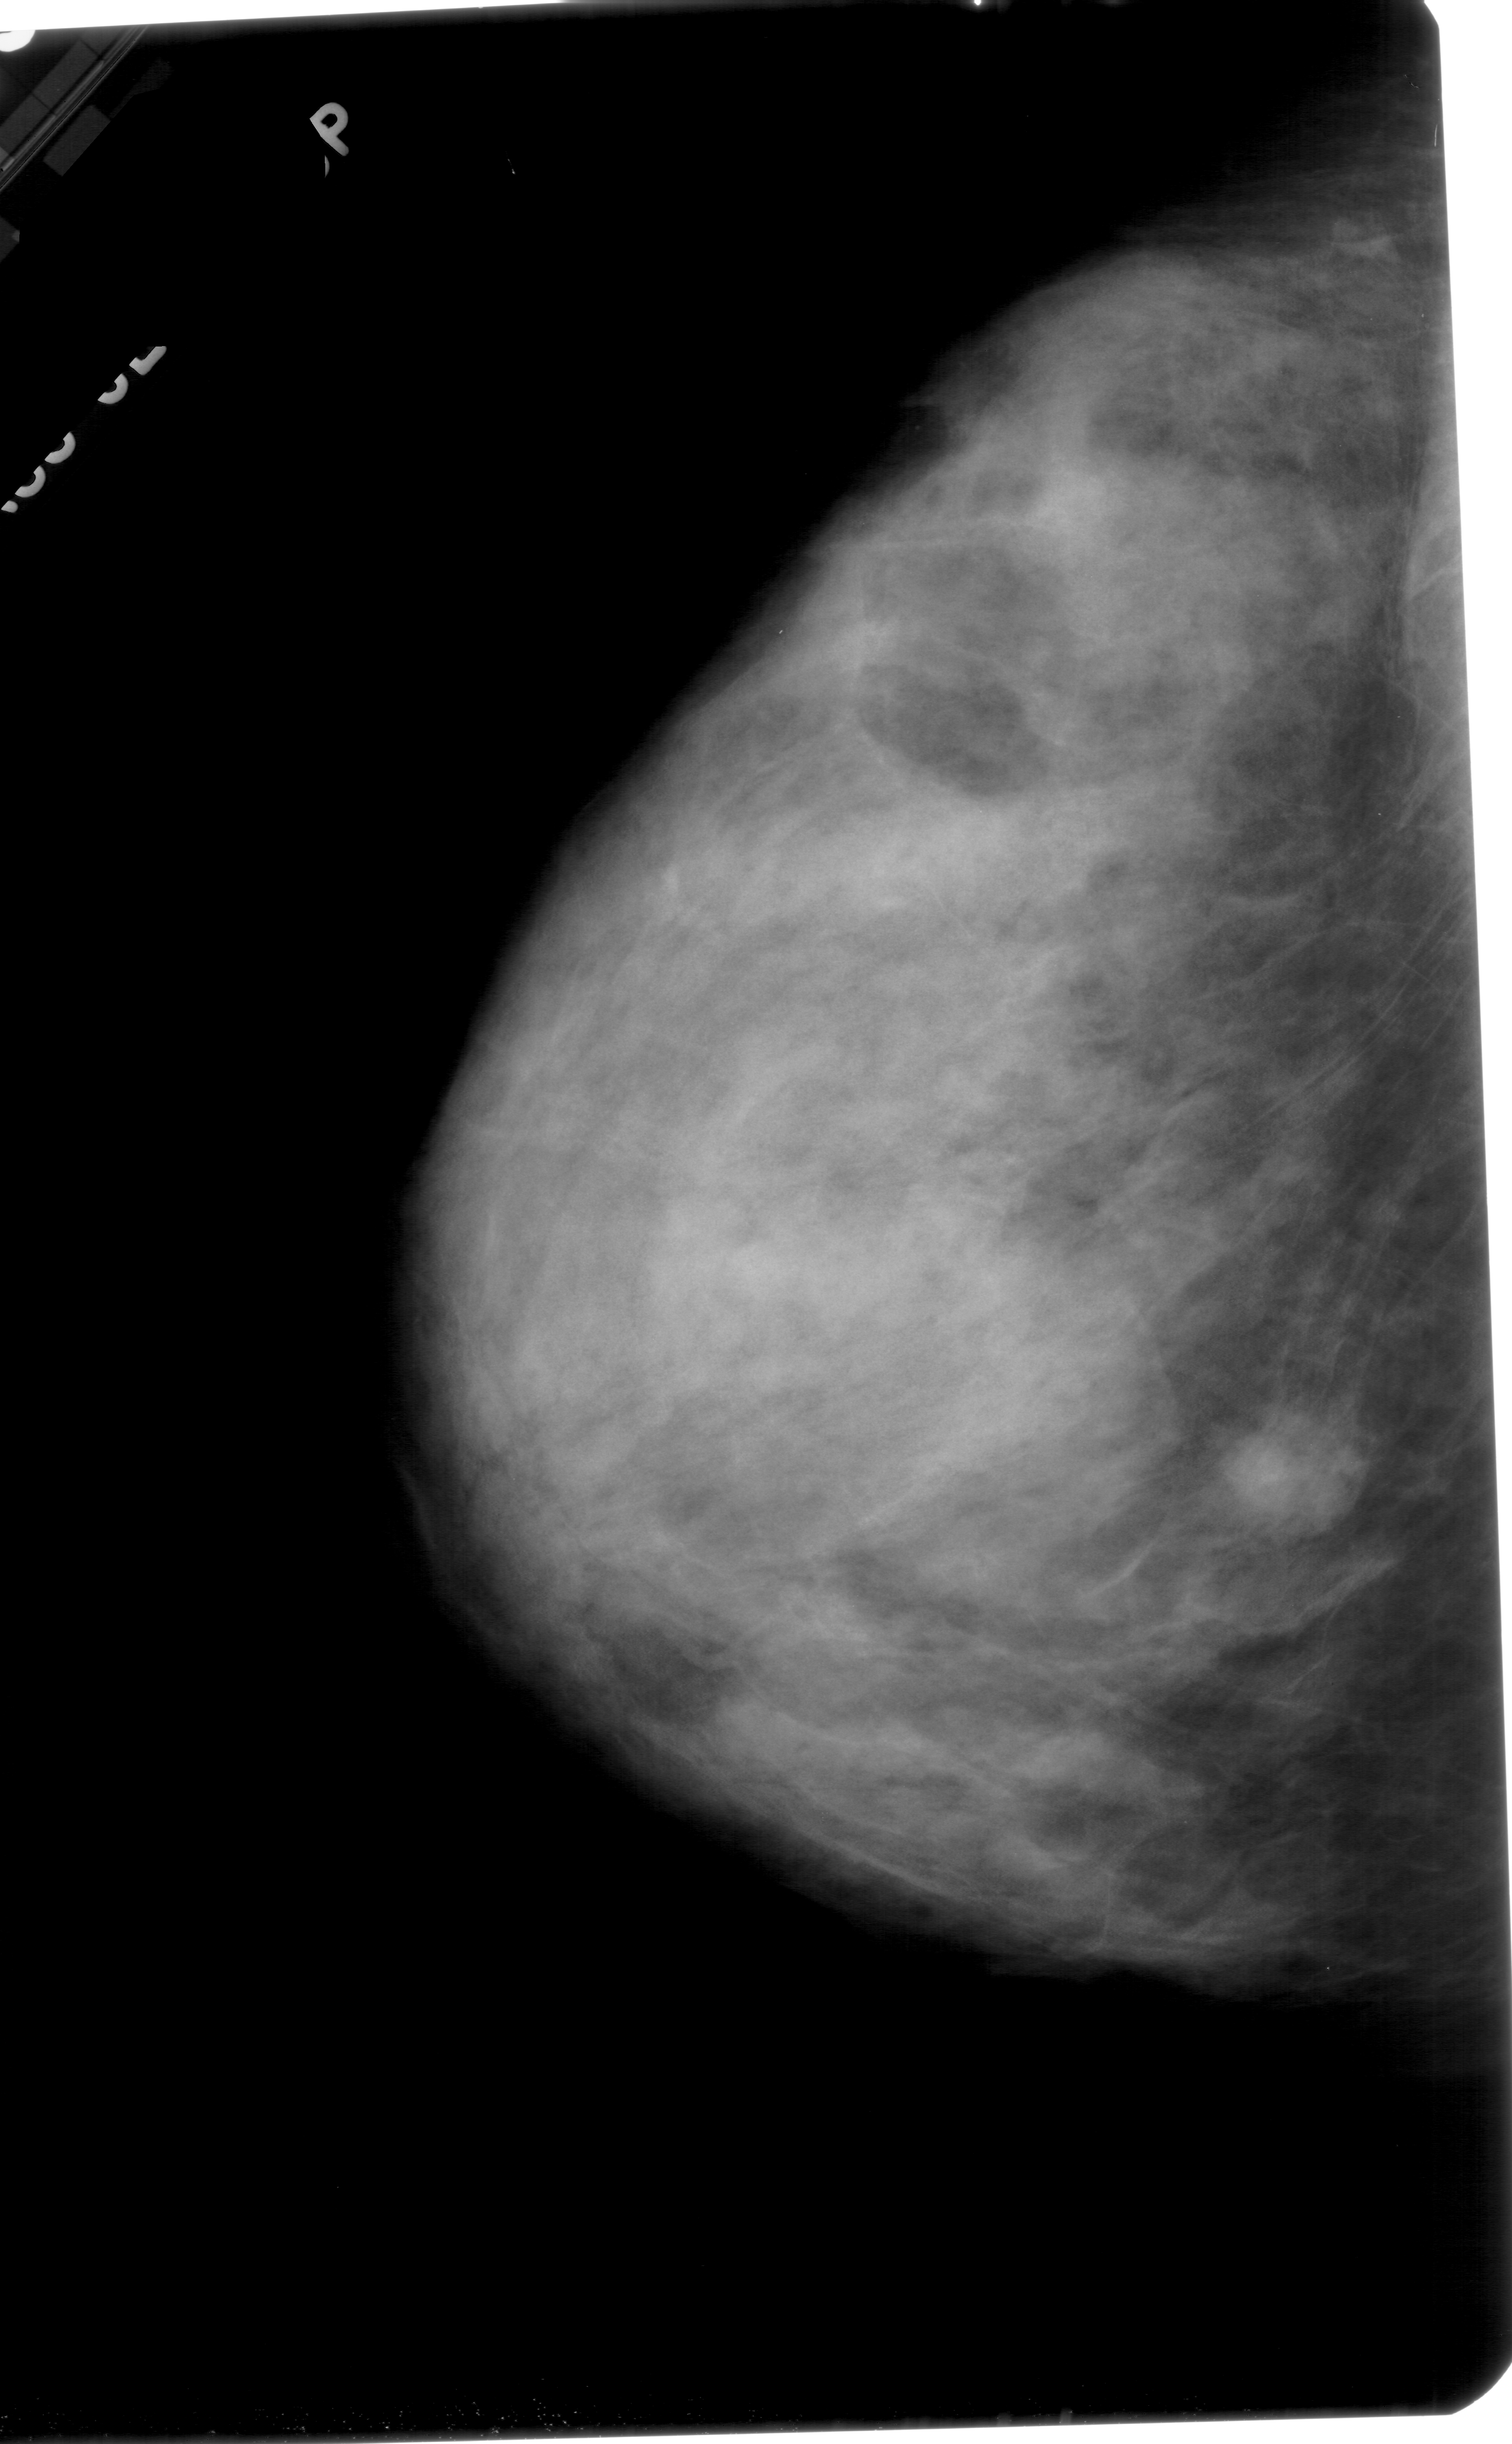
Digitized screen-film mammogram. Left breast. Craniocaudal (CC) view. Breast composition: extremely dense (BI-RADS density category 4 of 4). 1512 × 2444 image matrix.
Marked abnormalities (boxes around the expert regions of interest):
- mass, shape round, margins ill defined; BI-RADS assessment category 4; subtlety rating 3 on a 1 (subtle) to 5 (obvious) scale; pathology result (as recorded, not read from the image): malignant: bounding box (x1, y1, x2, y2) in pixels: (1224, 1422, 1360, 1537)